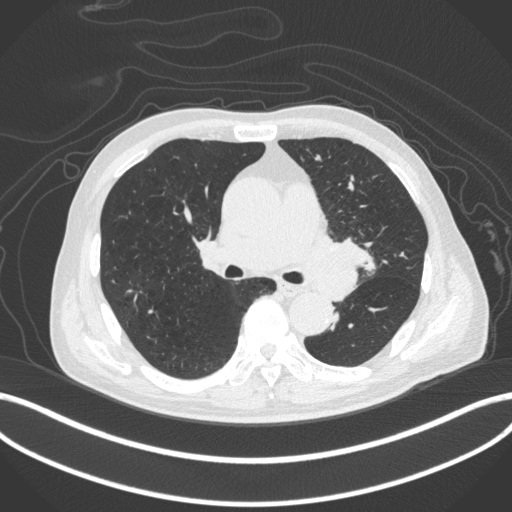
Chest CT, one axial slice. 120 kVp. Lung window (W 1500 / L -600 HU). 1 mm slice thickness. 512 × 512 image matrix, field of view 400 × 400 mm. Male patient, age 77 years. Case-level facts recorded for this patient, not image findings: clinical TNM (as recorded): T3 N1 M0.
Structures marked on this image (bounding box drawn by a radiologist):
- lung tumour (recorded histology: adenocarcinoma): box from (x=296, y=225) to (x=375, y=300) px